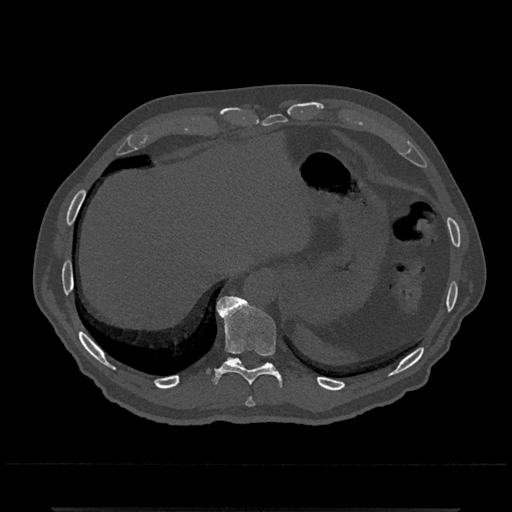
CT including the spine, one axial slice; position 549 of 797 along the scan axis; bone window (W 1800 / L 400 HU); 0.5 mm slice thickness; 512 × 512 image matrix, field of view 393 × 393 mm. Male patient, age 67 years. Case-level facts recorded for this patient, not image findings: primary cancer: prostate.
Annotated regions visible in this slice (semi-automatically segmented with operator editing):
- T10 vertebra: bounding box [x1, y1, x2, y2] px = [207, 295, 280, 385]
- T11 vertebra: [227, 357, 241, 362]
- T9 vertebra: [245, 398, 255, 407]